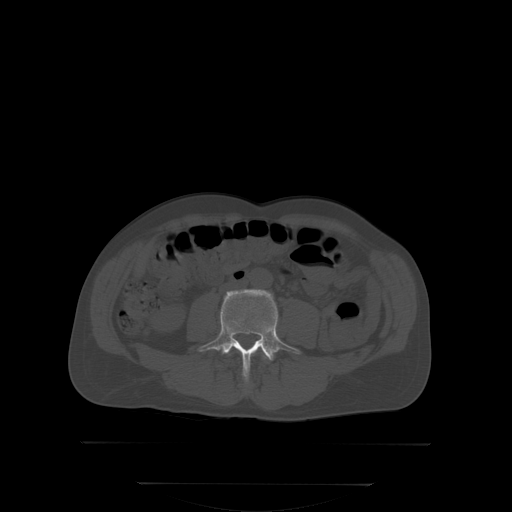
CT including the spine, one axial slice; position 111 of 350 along the scan axis; bone window (W 1800 / L 400 HU); 2.5 mm slice thickness; 512 × 512 image matrix. Male patient, age 58 years. Case-level facts recorded for this patient, not image findings: primary cancer: prostate; vertebrae with lytic lesions (as recorded): L1.
Structures marked on this image (semi-automatic segmentation, software-assisted and operator-edited):
- L3 vertebra: box from (x=263, y=355) to (x=266, y=358) px
- L4 vertebra: (x=198, y=290)–(x=301, y=384)